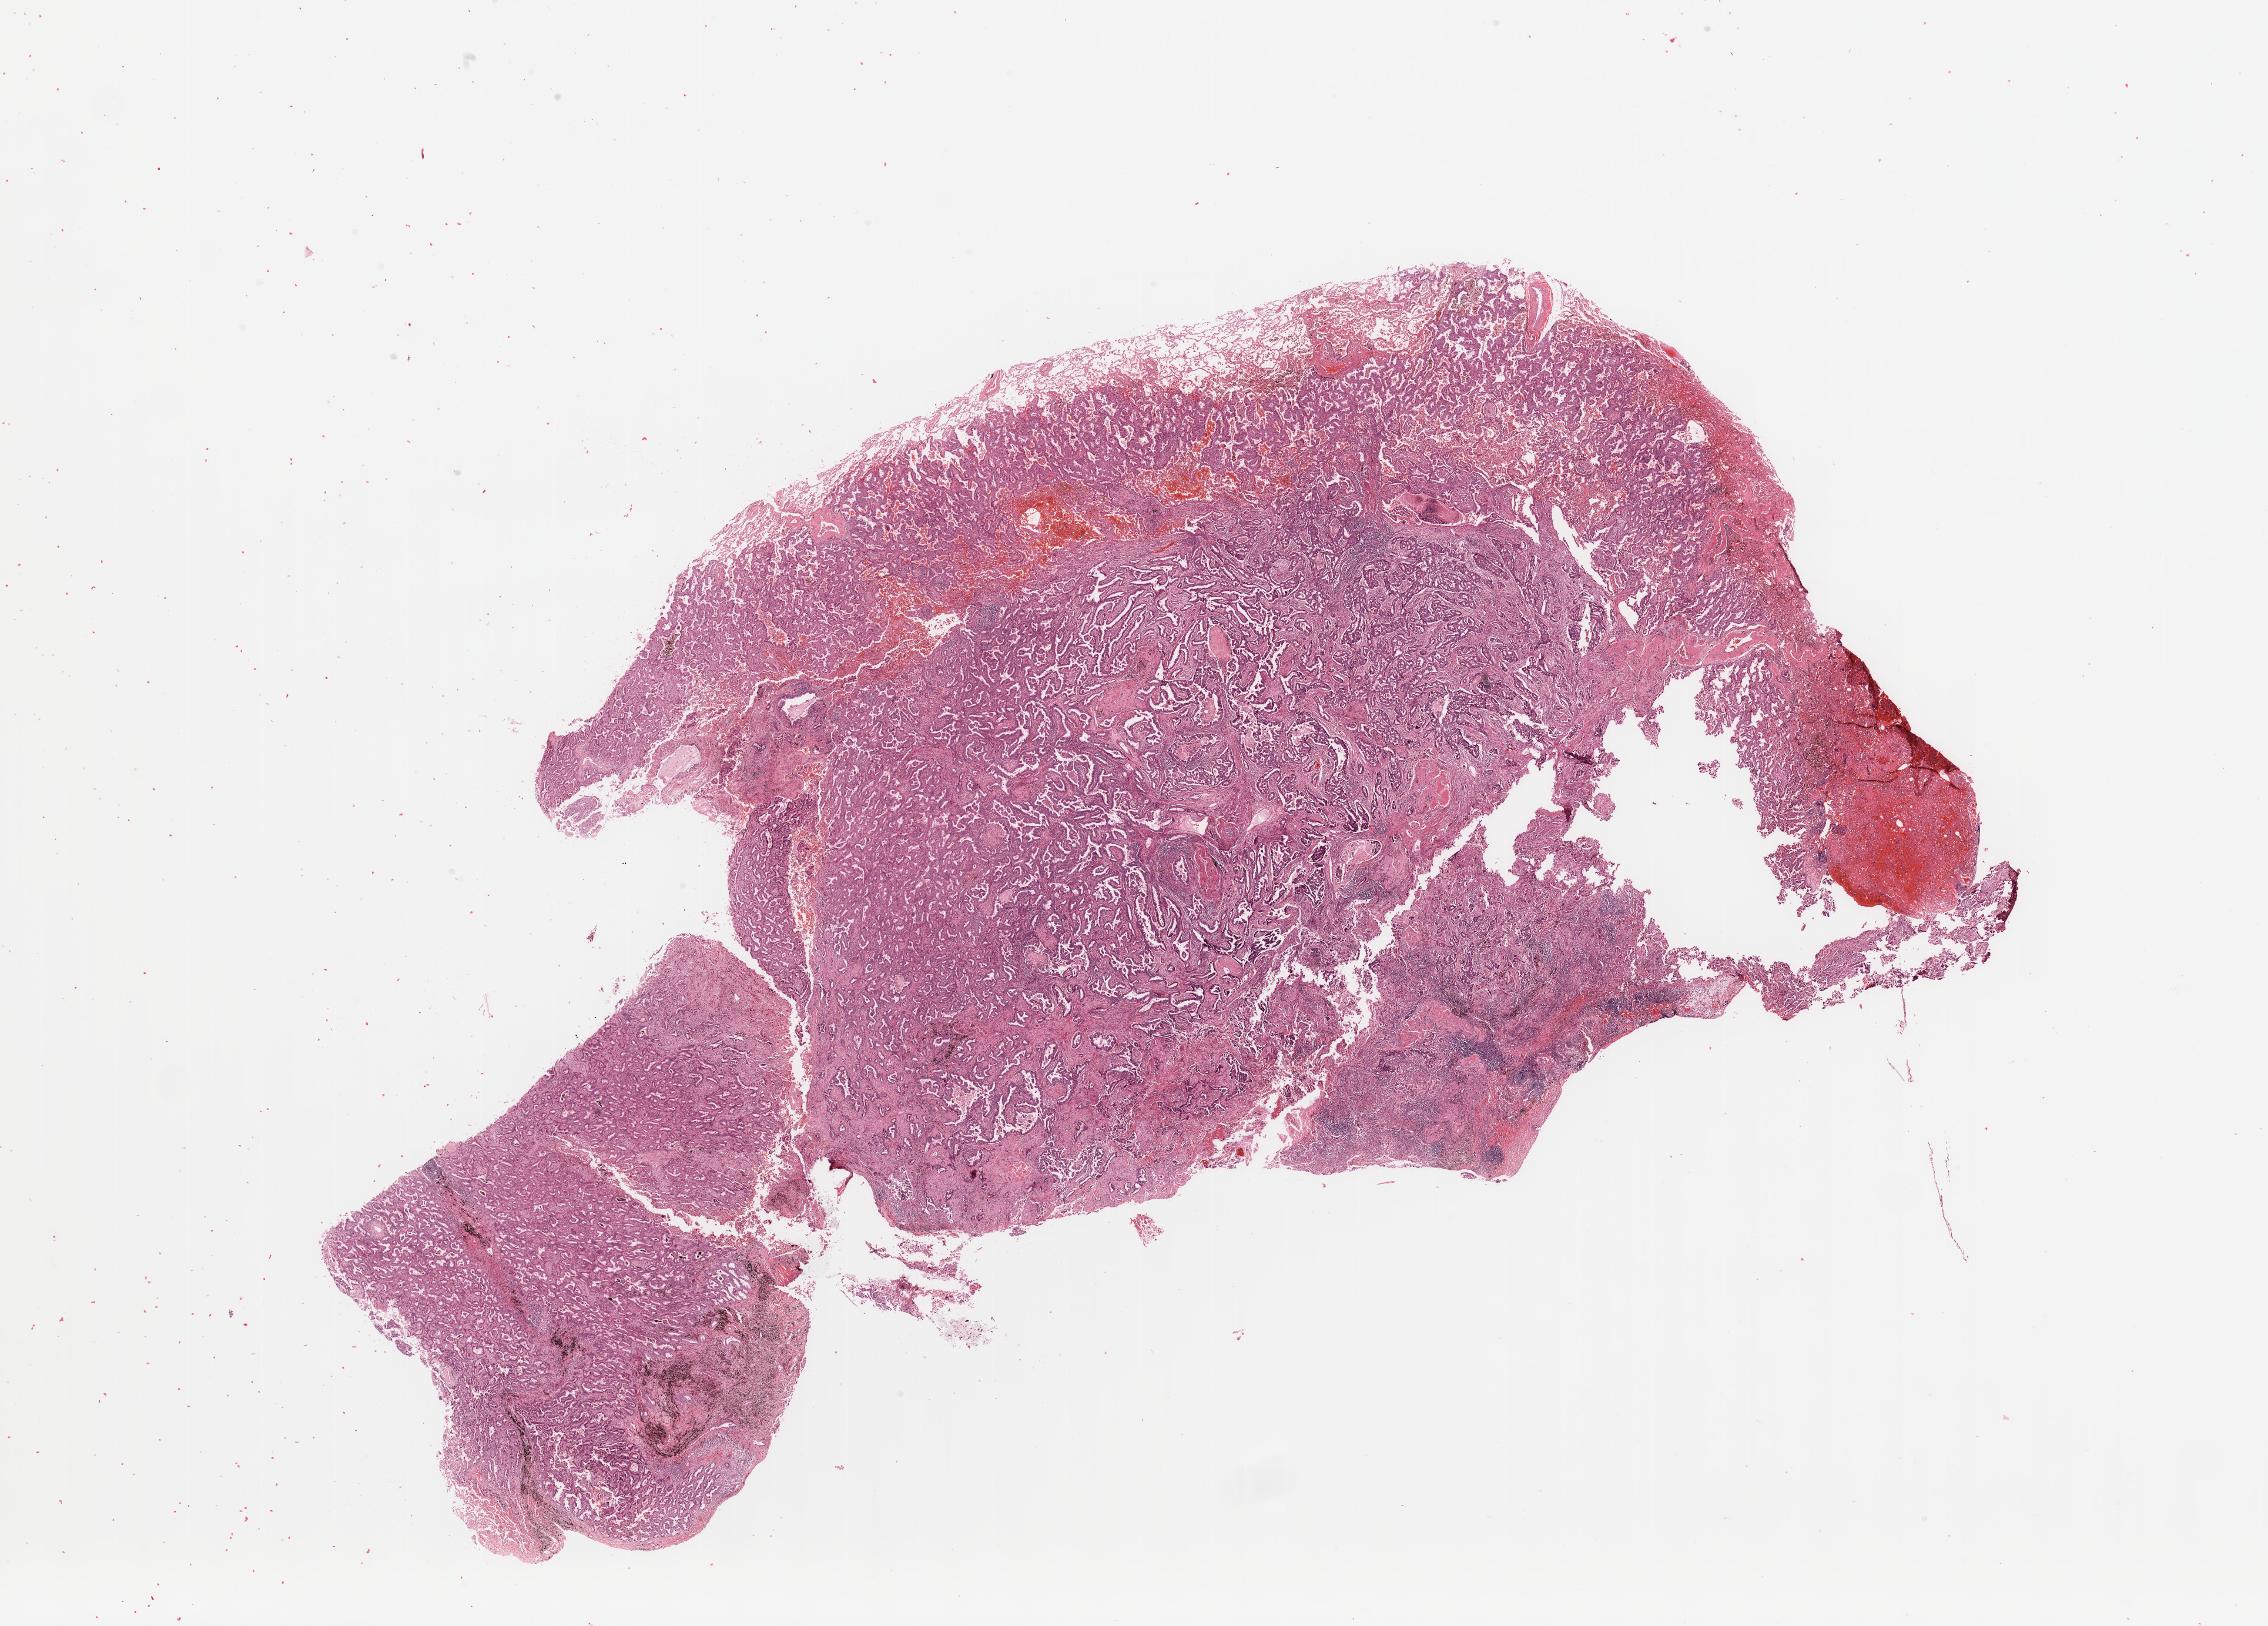
Whole-slide histology image, Hematoxylin and eosin (H&E) stained — a low-resolution overview of the entire scanned area, about 30.5 x 21.9 mm, lung, tumour tissue. 68-year-old female patient. Histologic grade: G2 (moderately differentiated).
* AJCC pathologic stage: IB
* histologic diagnosis: Adenocarcinoma, NOS